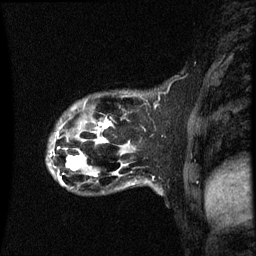
Breast MRI (dynamic contrast-enhanced), one sagittal slice. Slice 13 of 60 in the series (ordered by position). Dynamic contrast-enhanced series, image 2 of 3 at this slice position (ordered by acquisition). 1.5 T. TE 4.2 ms, TR 8.9 ms. 2 mm slice thickness. 256 × 256 image matrix. Female patient, age 44 years. From the clinical record (not read from this slice): setting: breast cancer imaged before/during neoadjuvant chemotherapy; receptor status: HR-positive, HER2-negative.
Outlined on this slice (semi-automatically segmented with operator editing):
- analysis volume of interest (the breast-tissue region the enhancement analysis was run in; not a lesion): bounding box (x1, y1, x2, y2) in pixels: (47, 94, 153, 189)
- tumour enhancement mask (voxels above the 70 % enhancement threshold inside the analysis volume of interest): (66, 122, 111, 171)